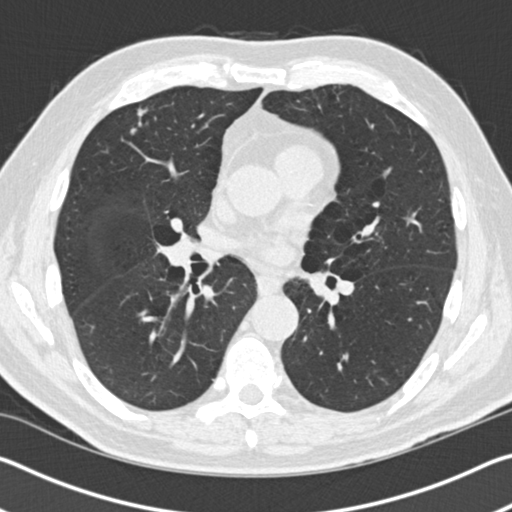
Axial slice from a low-dose chest CT screening exam. First (baseline) screen. Lung window (W 1500 / L -600 HU). 2 mm slice thickness. Standard (soft-tissue) reconstruction kernel (B30f). Male, age 69 years at enrolment.
- Expert reader's lesion annotation, bounding box <120,96,165,141> (left, top, right, bottom; pixels).
- No non-calcified nodule or mass ≥4 mm was recorded by the screening reader at this exam.
- Official screen result: negative screen, significant abnormalities not suspicious for lung cancer.
- Participant outcome: lung cancer diagnosed 545 days after this screen (after the second annual screen) — adenocarcinoma, NOS, right upper lobe, moderately differentiated (G2), stage IIA (AJCC 6th edition), 20 mm at pathology.